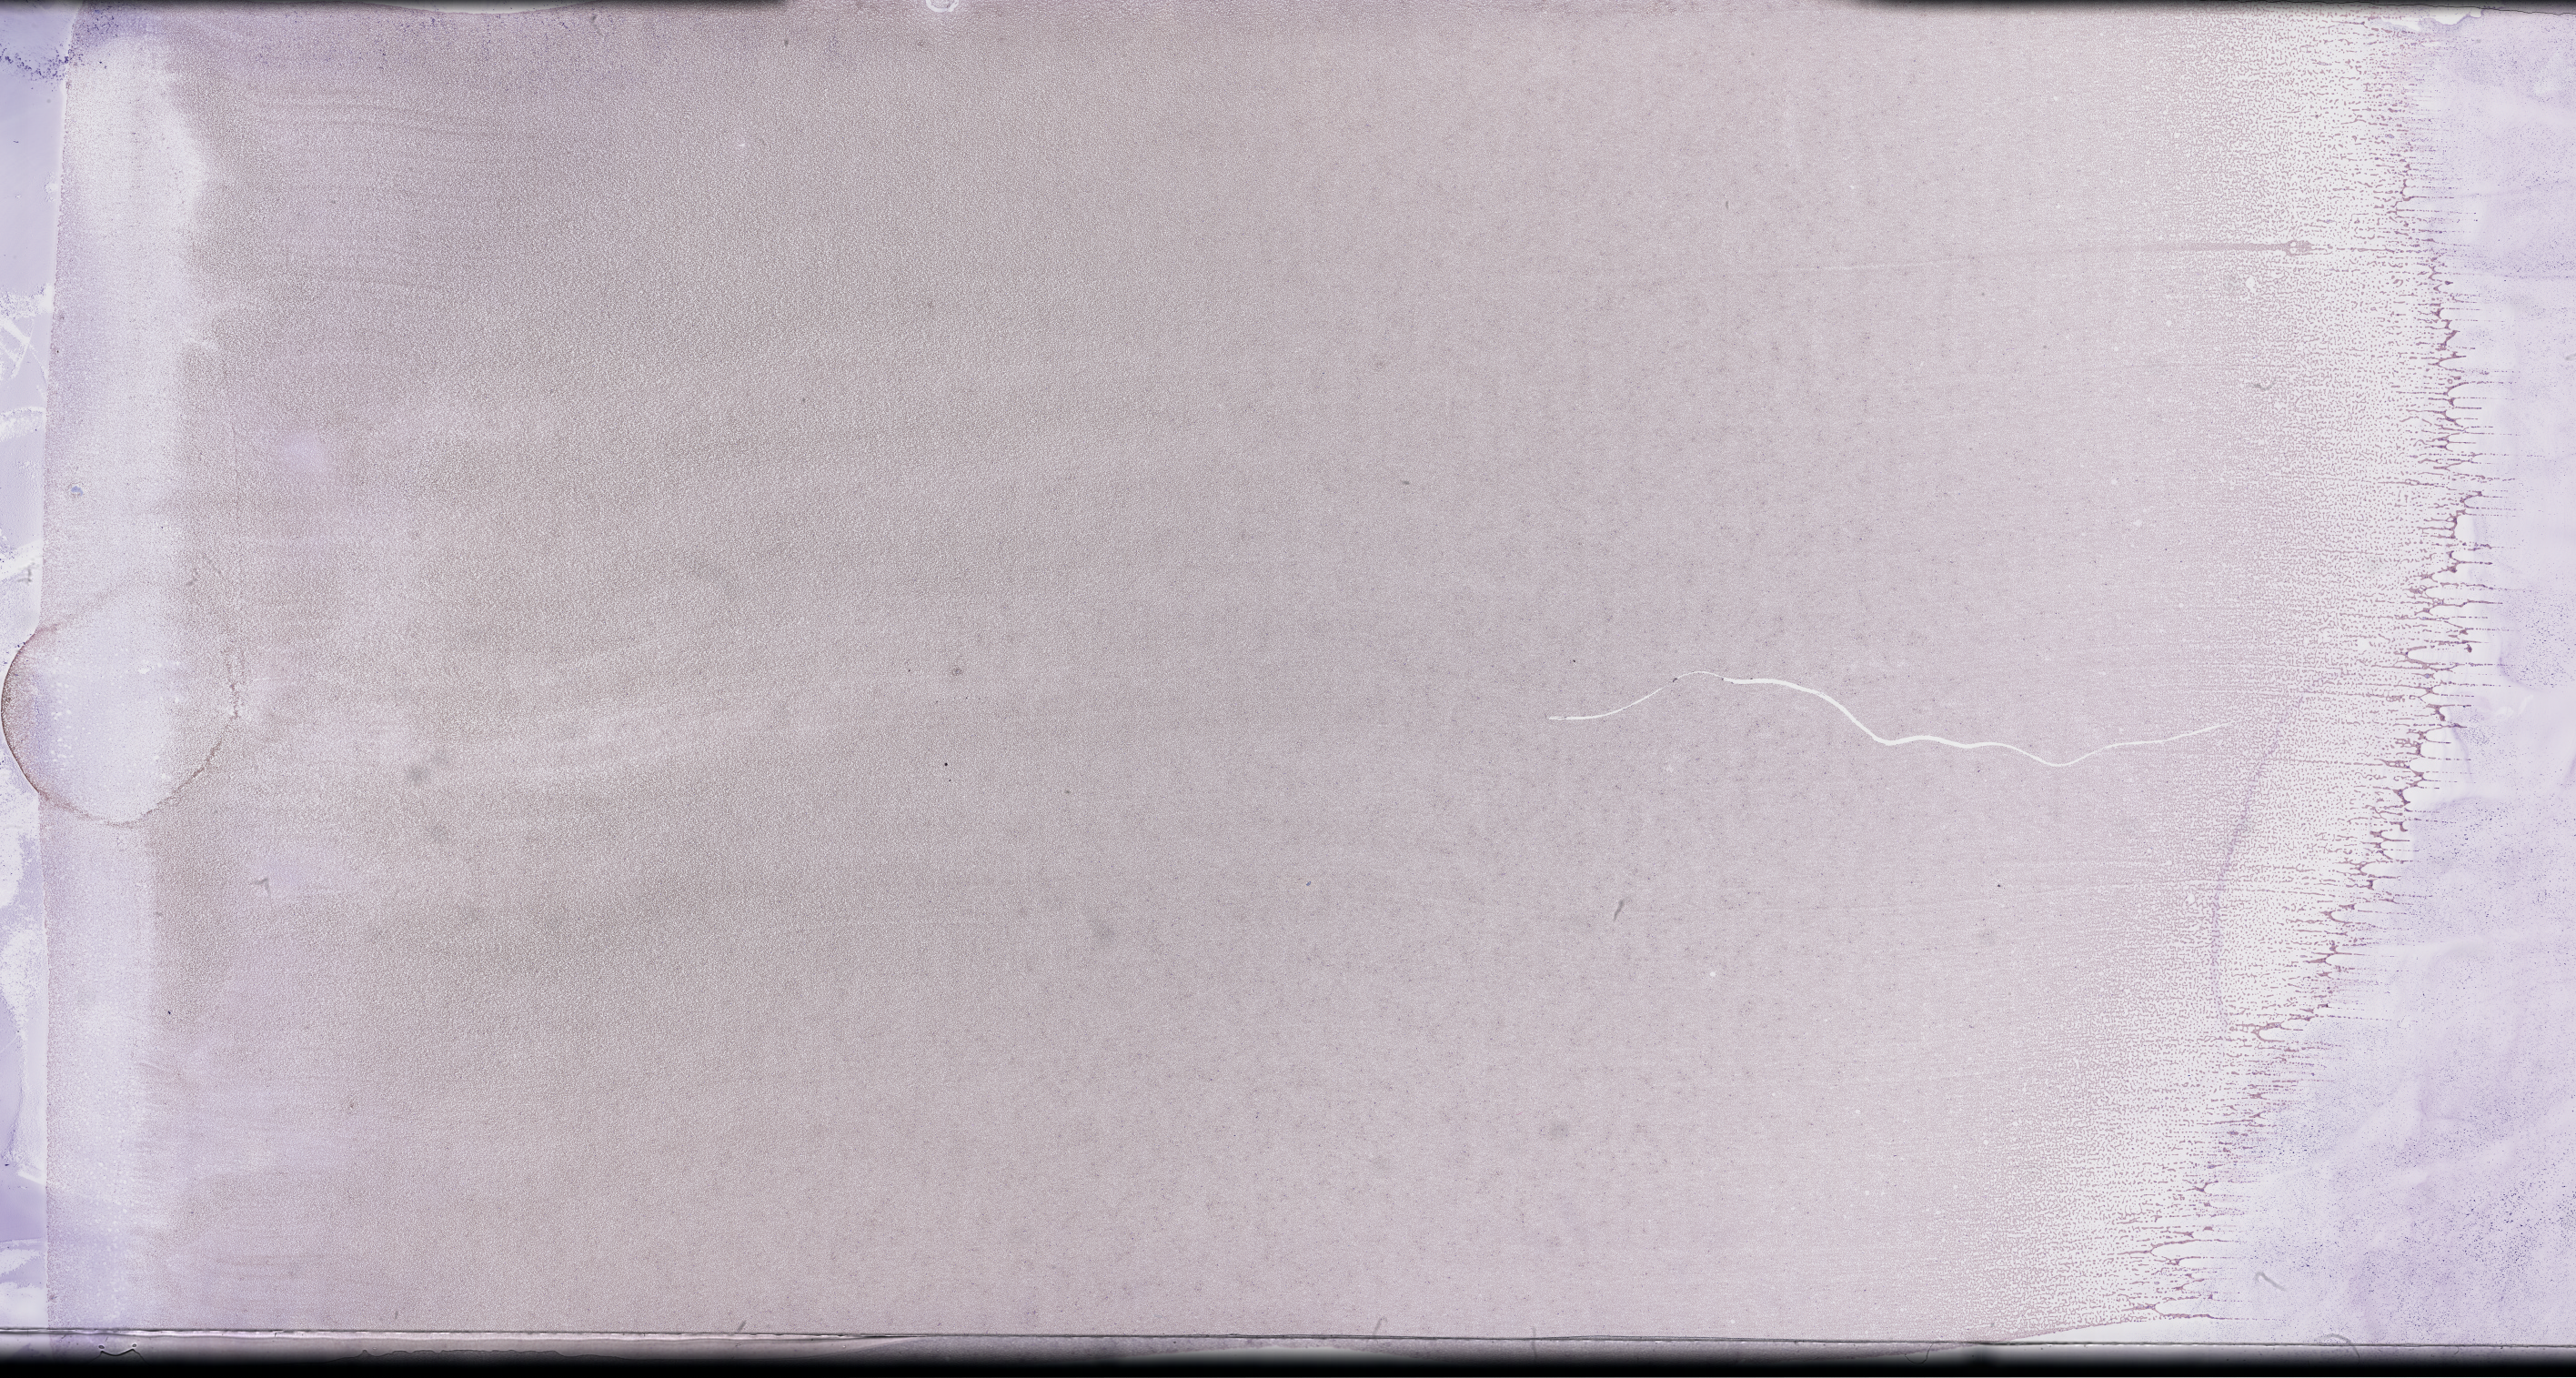
Whole-slide image of a whole blood smear, Wright-Giemsa stain, a low-resolution overview of the entire scanned area, about 45.7 x 24.5 mm, collected on treatment. Patient: female.
Patient diagnosis: Plasma Cell Myeloma.